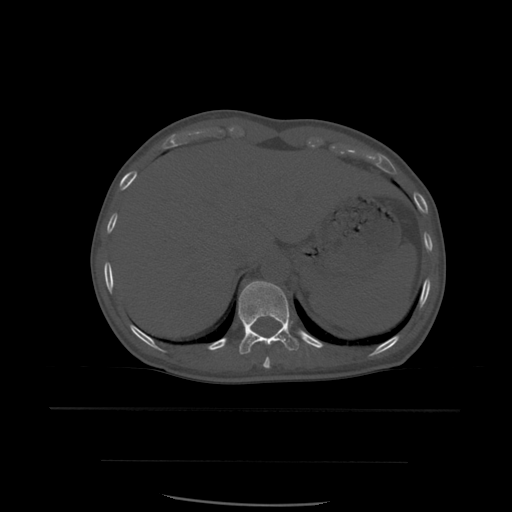
CT including the spine, one axial slice. Position 296 of 574 along the scan axis. Bone window (W 1800 / L 400 HU). 512 × 512 image matrix. Patient age 48 years. Case-level facts recorded for this patient, not image findings: primary cancer: lung; vertebrae with lytic lesions (as recorded): T11.
Annotated regions visible in this slice (semi-automatically segmented with operator editing):
- T10 vertebra: bounding box [x1, y1, x2, y2] px = [263, 357, 271, 369]
- T11 vertebra: [238, 281, 300, 355]